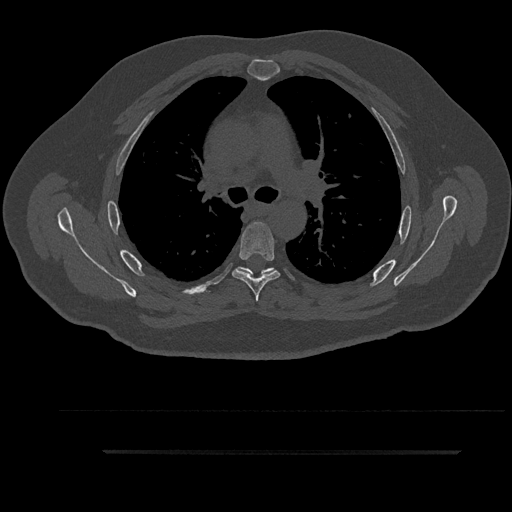
CT including the spine, one axial slice. Position 621 of 797 along the scan axis. Reconstruction kernel Br40s/3. Bone window (W 1800 / L 400 HU). 0.5 mm slice thickness. 512 × 512 image matrix, field of view 432 × 432 mm. Male patient, age 63 years. From the clinical record (not read from this slice): primary cancer: renal.
Structures marked on this image (semi-automatically segmented with operator editing):
- T5 vertebra: bounding box (x1, y1, x2, y2) in pixels: (232, 222, 280, 301)
- T6 vertebra: (240, 267, 276, 279)